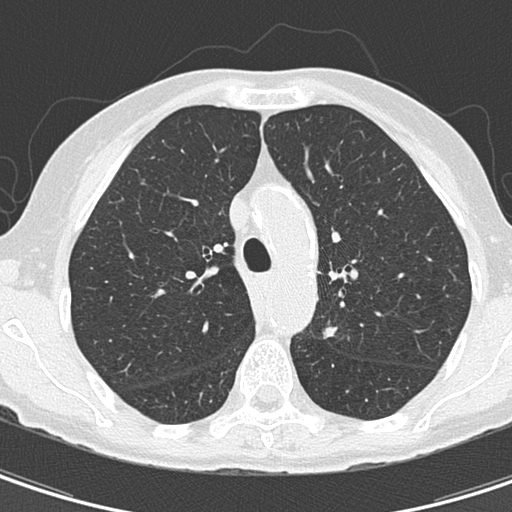
Axial slice from a low-dose chest CT screening exam. First (baseline) screen. Lung window (W 1500 / L -600 HU). 2 mm slice thickness. 120 kVp. Female, age 67 years at enrolment.
Expert reader's lesion annotation, bounding box (x1, y1, x2, y2) in pixels: (296, 311, 359, 359). The exam's reader record, not a measurement of the box and not confirmed to be the same lesion: non-calcified nodule or mass ≥4 mm, left upper lobe, 11 × 8 mm, spiculated (stellate) margins, soft tissue attenuation. Later outcome: lung cancer diagnosed 73 days after this screen — adenocarcinoma, NOS, left upper lobe, poorly differentiated (G3), stage IA (AJCC 6th edition), 13 mm at pathology.